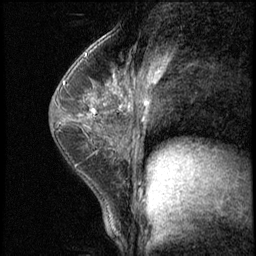
Breast MRI (dynamic contrast-enhanced), one sagittal slice; slice 38 of 62 in the series (ordered by position); 3 images stored at this slice position (order not interpretable as contrast timing); 1.5 T; TE 4.2 ms, TR 8.7 ms; 2.5 mm slice thickness; 256 × 256 image matrix, field of view 180 × 180 mm. Patient: female, 35 years. From the clinical record (not read from this slice): setting: breast cancer imaged before/during neoadjuvant chemotherapy; receptor status: HER2-positive.
Outlined on this slice (semi-automatically segmented with operator editing):
- analysis volume of interest (the breast-tissue region the enhancement analysis was run in; not a lesion): bounding box <71,78,120,139> (left, top, right, bottom; pixels)
- tumour enhancement mask (voxels above the 140 % enhancement threshold inside the analysis volume of interest): <91,108,96,112>